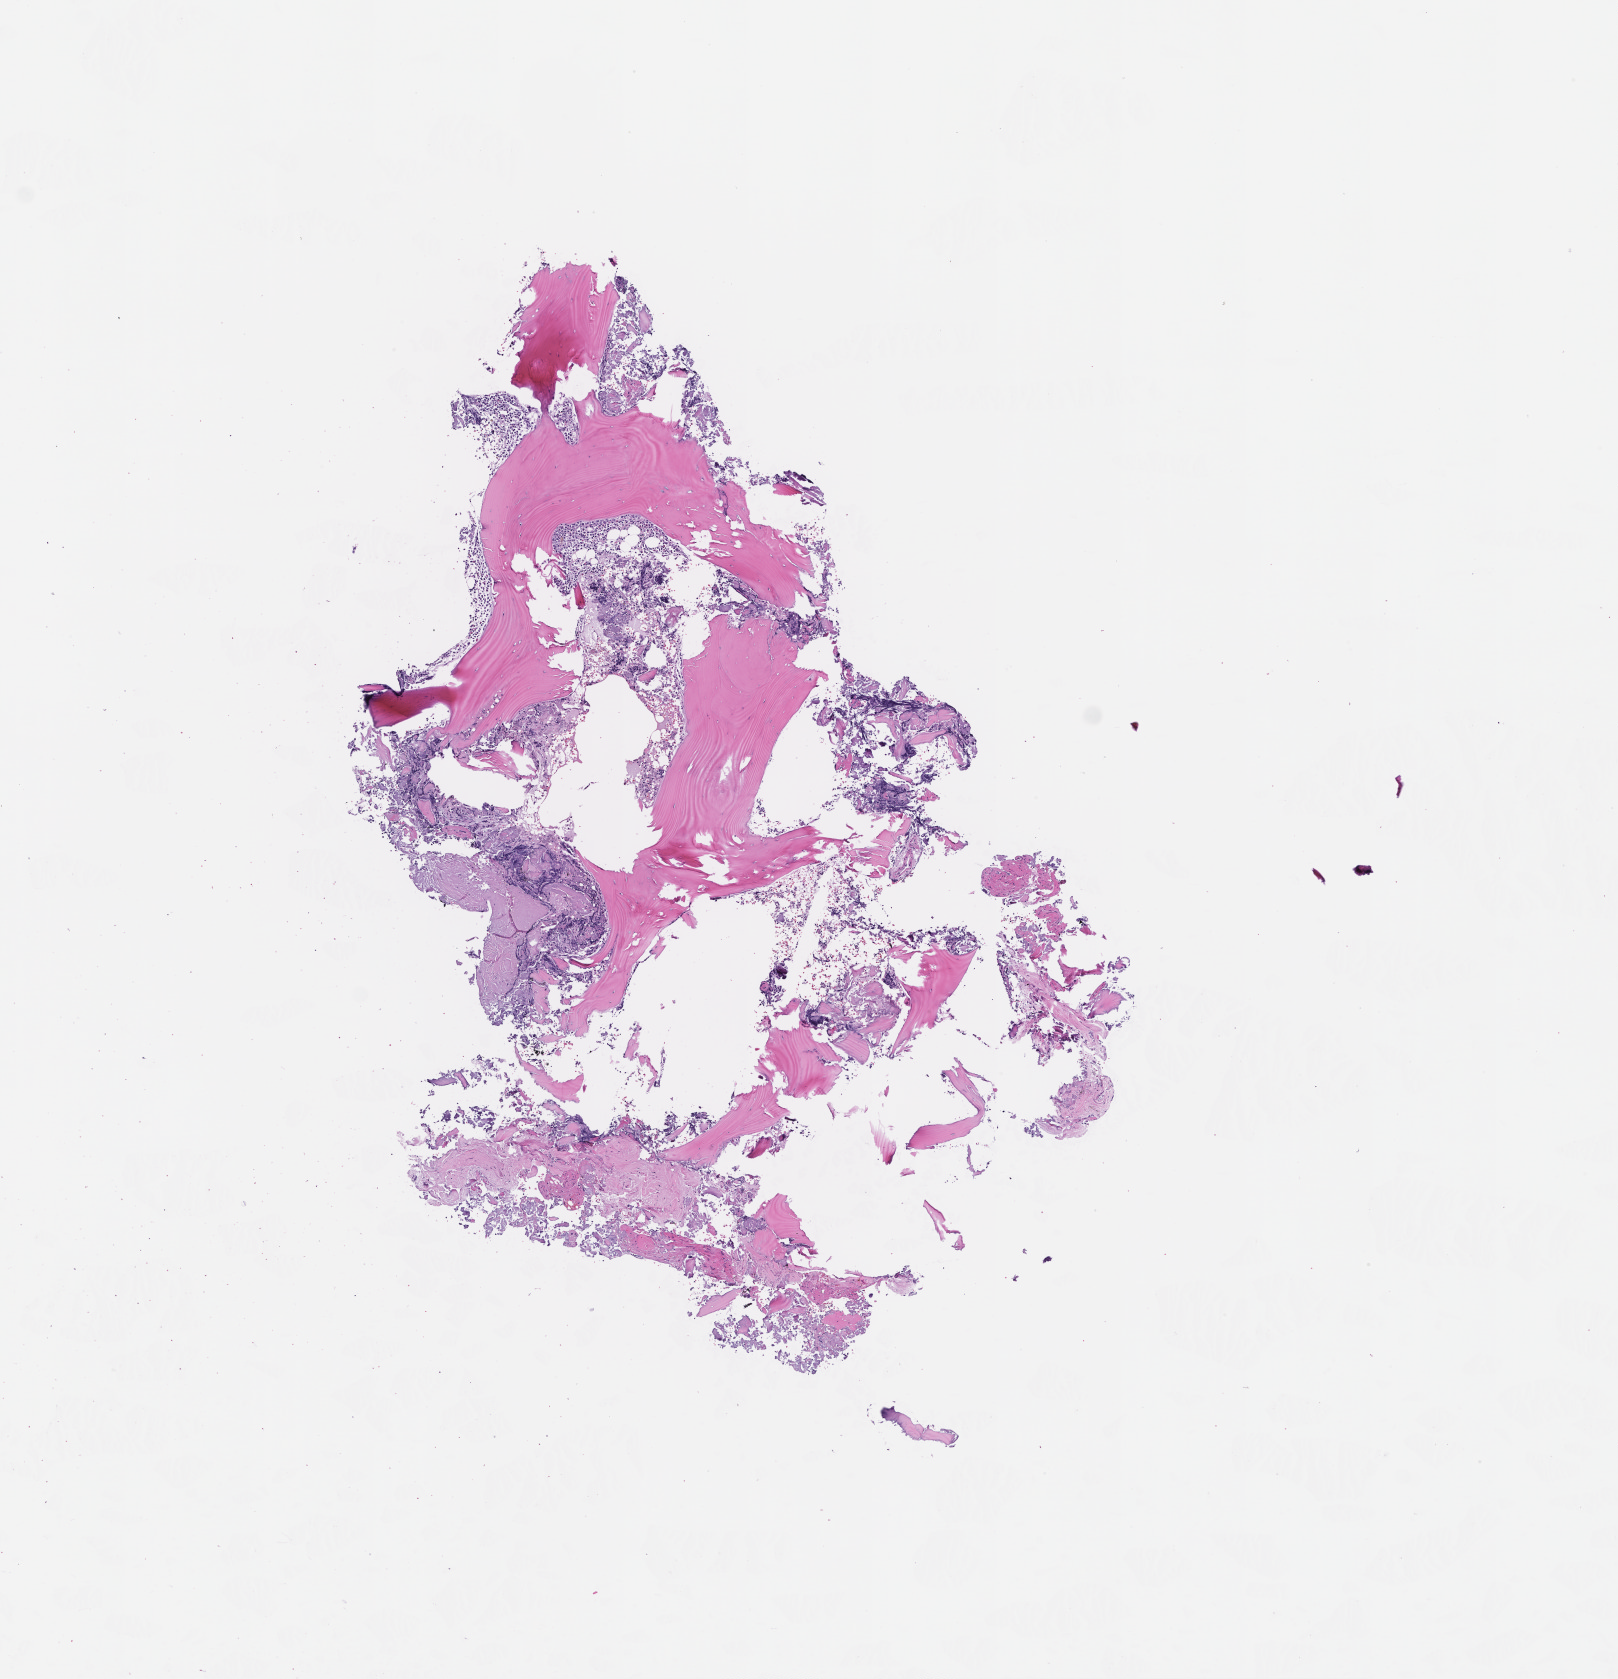
Digitized H&E-stained section — whole scanned area (about 6.5 x 6.8 mm) shown as a low-resolution overview. FFPE section. Site: bone marrow. Female patient.
This section: primary tumour tissue. Diagnosis: Acute Myeloid Leukemia Not Otherwise Specified.